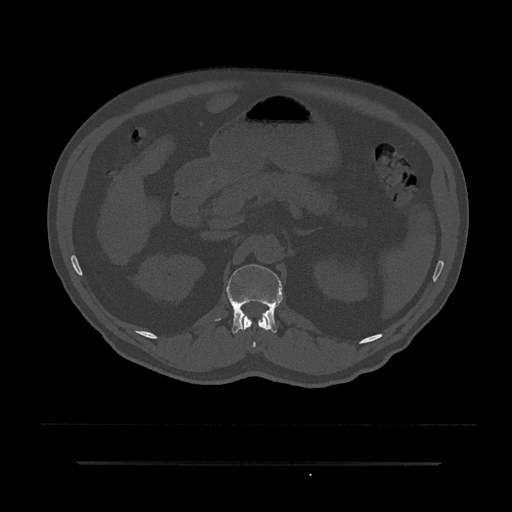
CT including the spine, one axial slice. Slice 169 of 797 in the series (ordered by position). Bone window (W 1800 / L 400 HU). 0.5 mm slice thickness. 512 × 512 image matrix, field of view 464 × 464 mm. Male patient, age 59 years. From the clinical record (not read from this slice): primary cancer: bile ducts; vertebrae with lytic lesions (as recorded): T10.
Annotated regions visible in this slice (semi-automatic segmentation, software-assisted and operator-edited):
- L1 vertebra: bounding box [x1, y1, x2, y2] px = [216, 264, 283, 334]
- T12 vertebra: [241, 315, 268, 349]